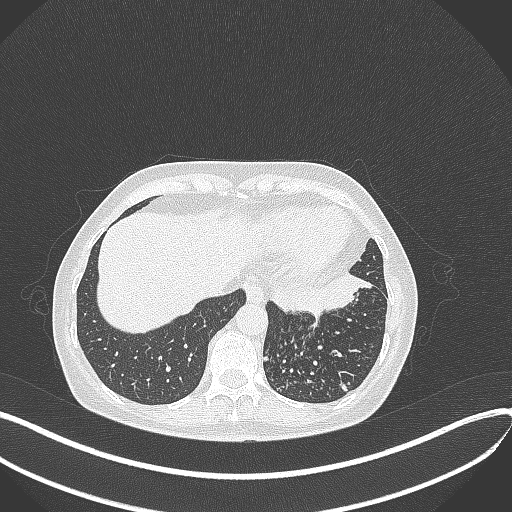
Chest CT, one axial slice. Position 94 of 429 along the scan axis. Reconstruction kernel B70f. Lung window (W 1500 / L -600 HU). 512 × 512 image matrix. Patient: female, 63 years. Case-level facts recorded for this patient, not image findings: clinical TNM (as recorded): T1b N0 M0.
Outlined on this slice (rectangle marked by the reading radiologist):
- lung tumour (recorded histology: adenocarcinoma): bounding box (x1, y1, x2, y2) in pixels: (268, 267, 376, 321)